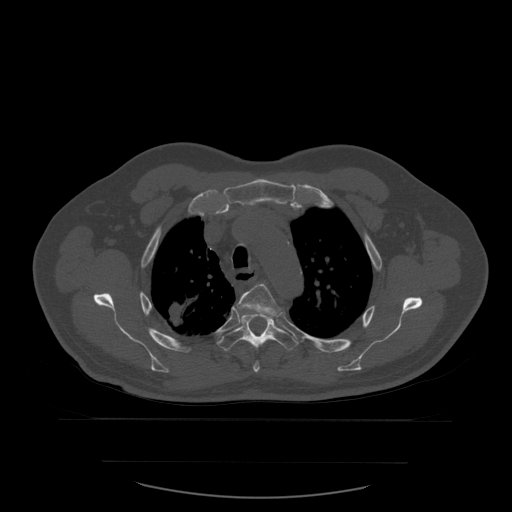
CT including the spine, one axial slice; bone window (W 1800 / L 400 HU); 1.25 mm slice thickness; 512 × 512 image matrix, field of view 479 × 479 mm. Patient age 71 years. Case-level facts recorded for this patient, not image findings: primary cancer: lung; vertebrae with lytic lesions (as recorded): T1, T2, L5, S1.
Outlined on this slice (semi-automatically segmented with operator editing):
- T4 vertebra: bounding box (x1, y1, x2, y2) in pixels: (237, 284, 281, 373)
- T5 vertebra: (217, 313, 299, 351)